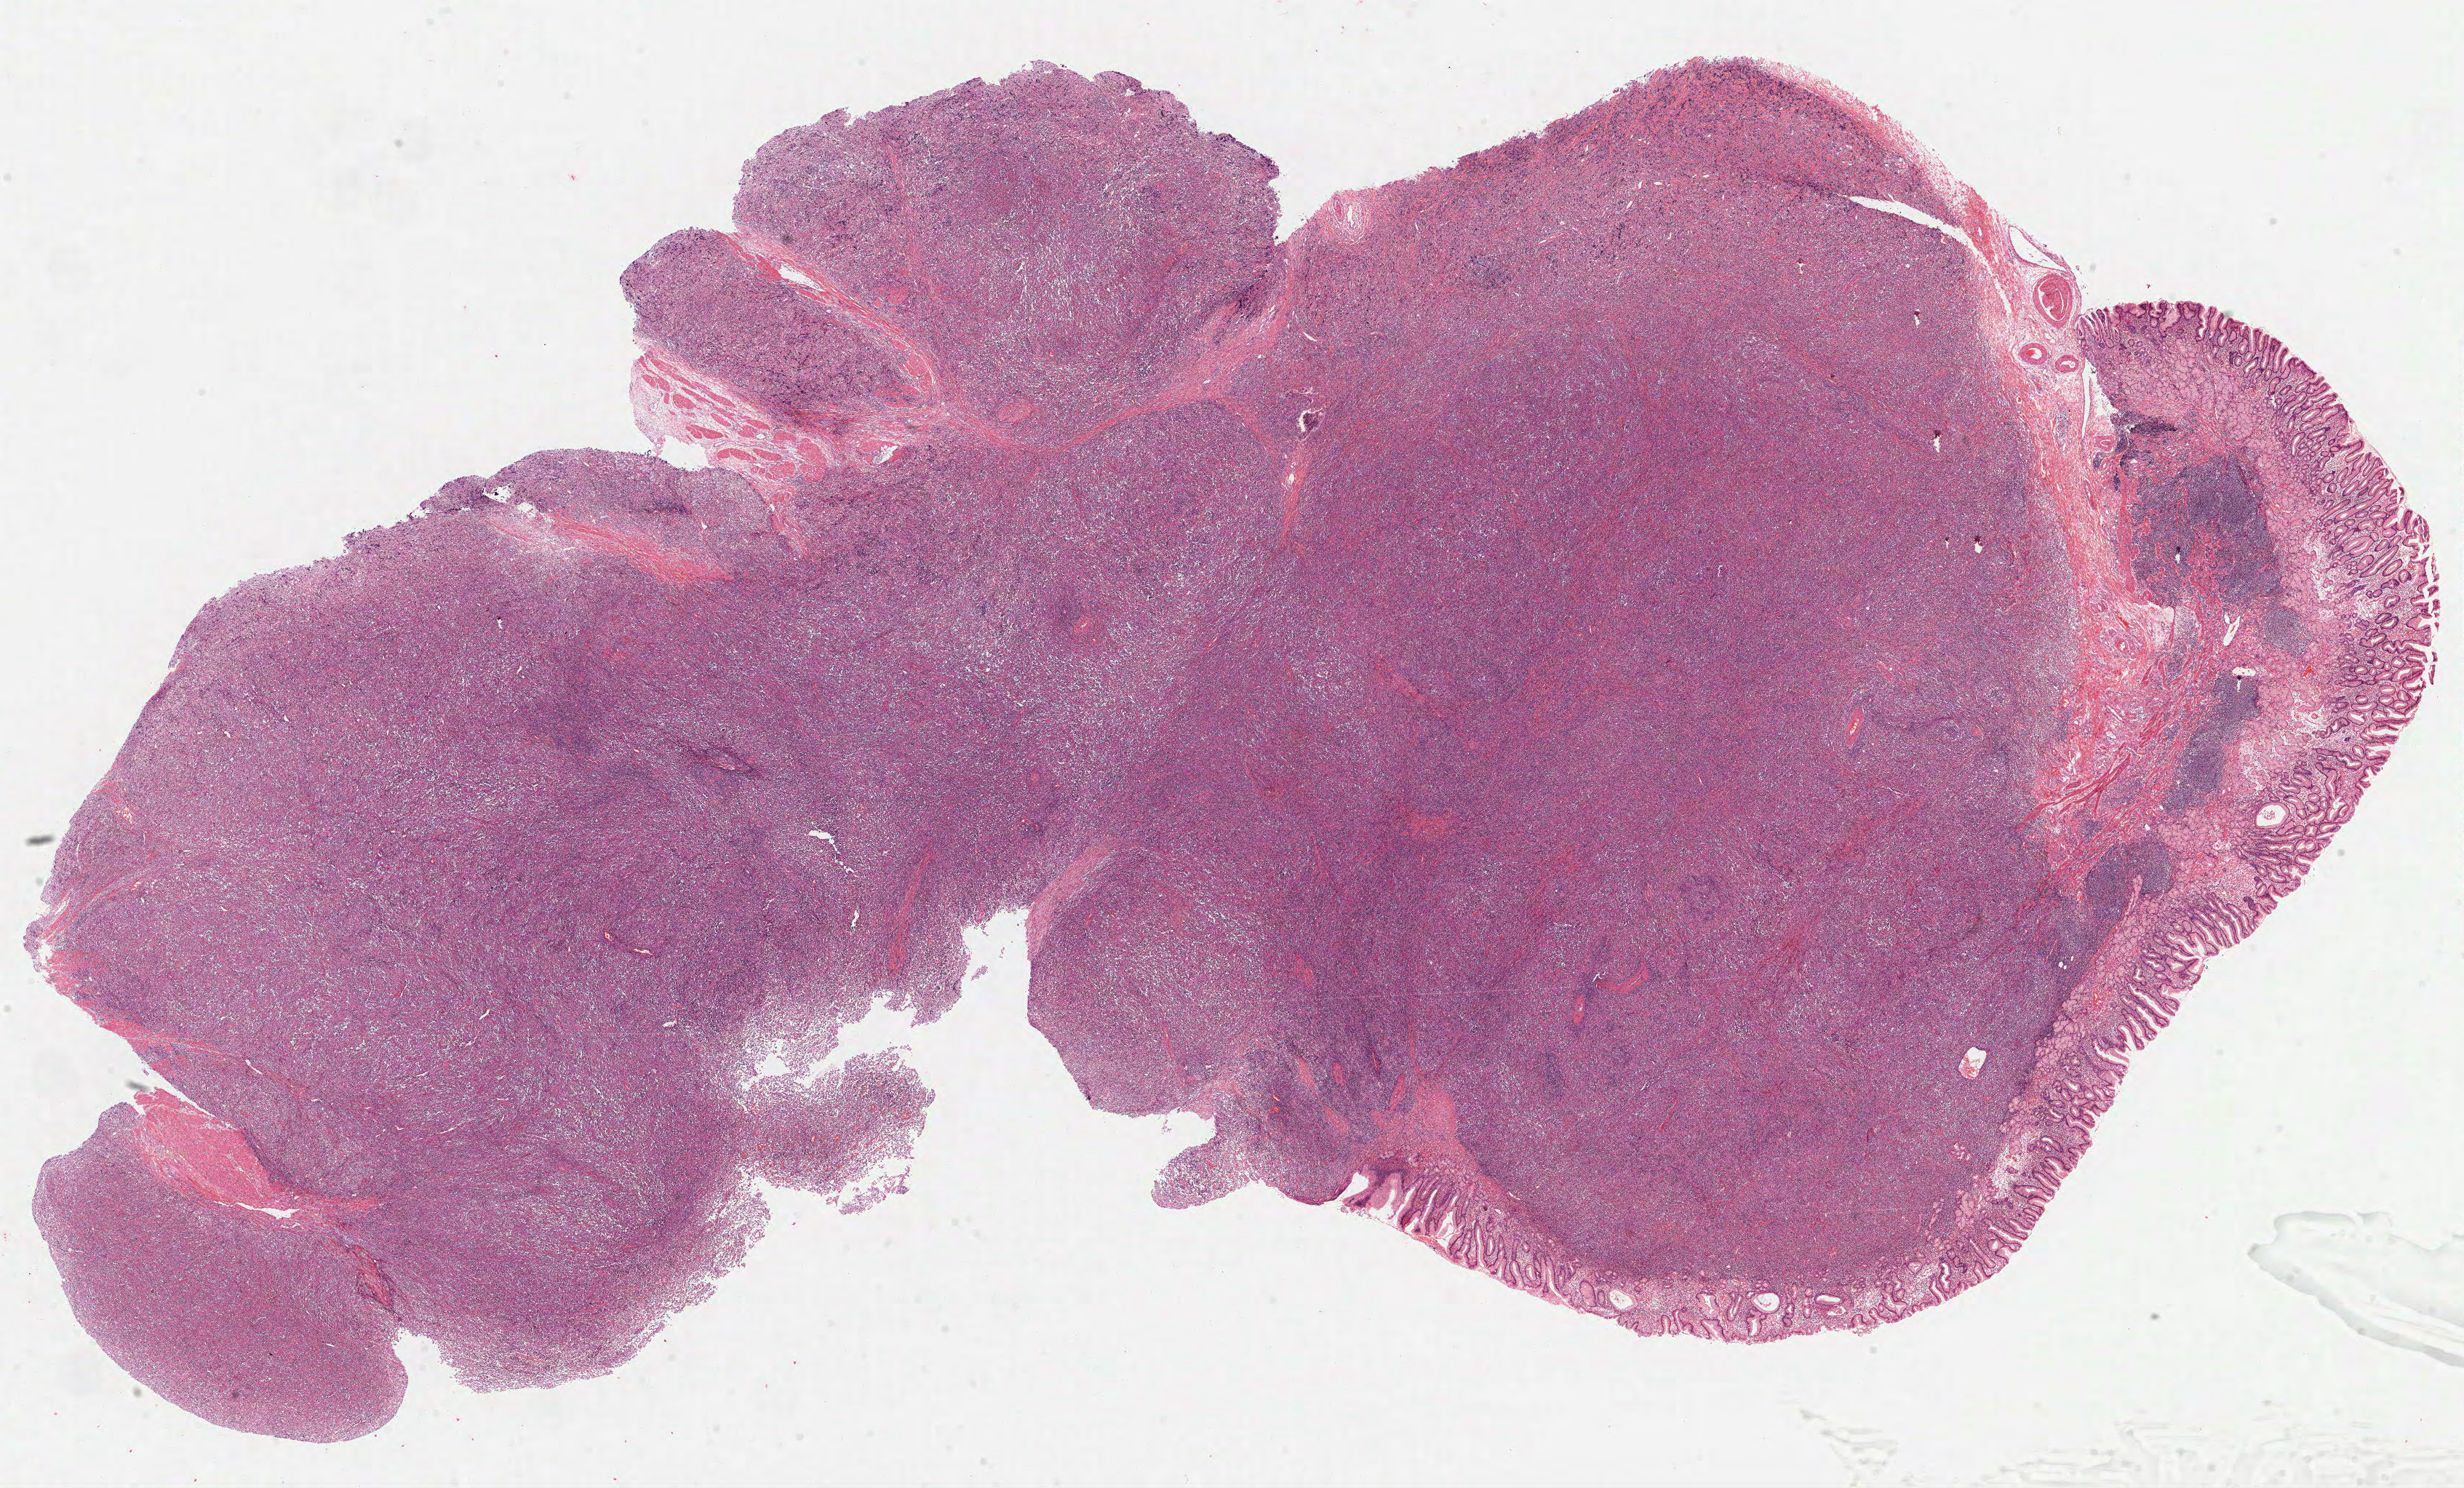
Hematoxylin and eosin (H&E) stained whole-slide image, shown as a low-resolution overview of the whole scanned area (about 27.3 x 16.5 mm). FFPE section. Primary tumour sample from the lymphoid tissue. Male patient; age at initial diagnosis 75 years.
- diagnosis: Diffuse large B-cell lymphoma, NOS (stomach, NOS)